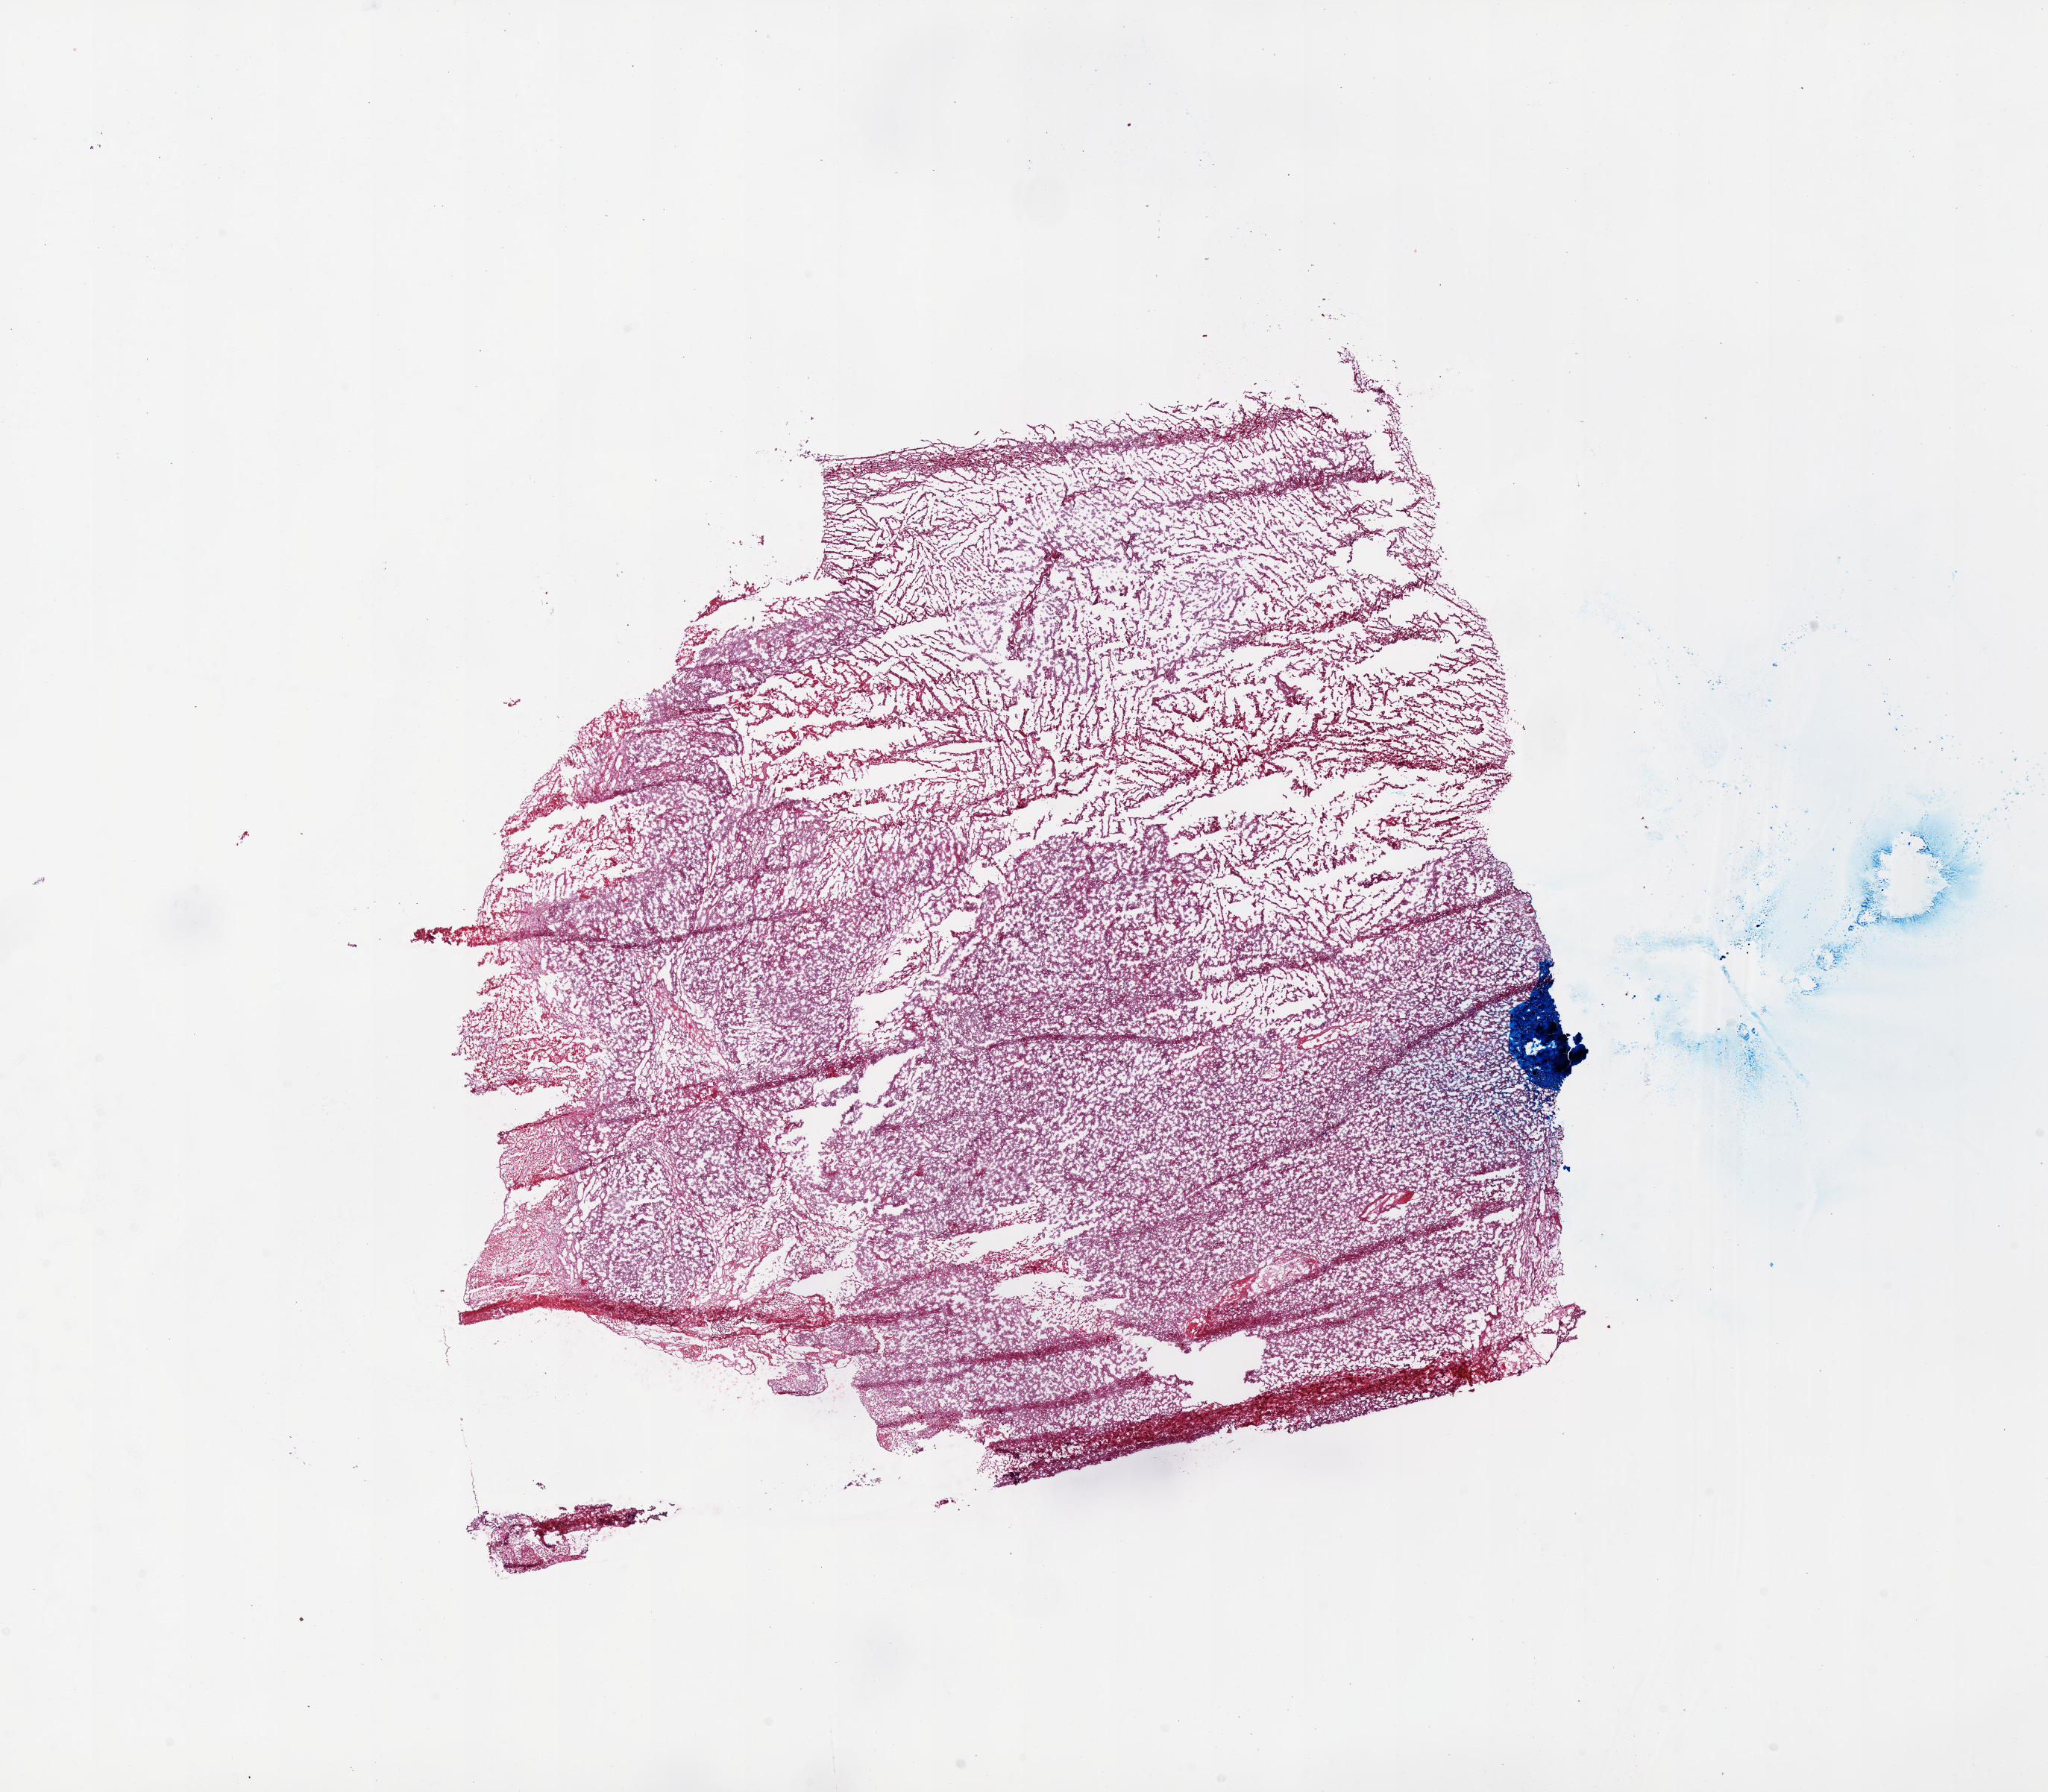
Digitized H&E tissue section (whole slide), whole scanned area (about 22.0 x 19.2 mm) shown as a low-resolution overview; frozen section from the top of the tissue portion; sample: primary tumour, brain. Male patient; age at initial diagnosis 40 years. Composition of this section per pathologist review: tumour cells 75%, tumour nuclei 100%, normal cells 0%, stromal cells 0%, necrosis 25%. Infiltration values recorded for this section: lymphocyte infiltration 0%.
Pathologic diagnosis: Glioblastoma.